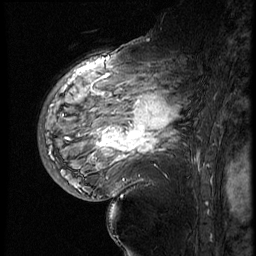
Breast MRI (dynamic contrast-enhanced), one sagittal slice. Position 40 of 60 along the scan axis. 4 images stored at this slice position (order not interpretable as contrast timing). 1.5 T. TE 4.2 ms, TR 9 ms. 2.5 mm slice thickness. 256 × 256 image matrix, field of view 180 × 180 mm. Female patient, age 56 years. From the clinical record (not read from this slice): setting: breast cancer imaged before/during neoadjuvant chemotherapy; receptor status: HER2-positive.
Outlined on this slice (semi-automatic segmentation, software-assisted and operator-edited):
- analysis volume of interest (the breast-tissue region the enhancement analysis was run in; not a lesion): bounding box (x1, y1, x2, y2) in pixels: (82, 83, 199, 177)
- tumour enhancement mask (voxels above the 140 % enhancement threshold inside the analysis volume of interest): (96, 95, 179, 162)